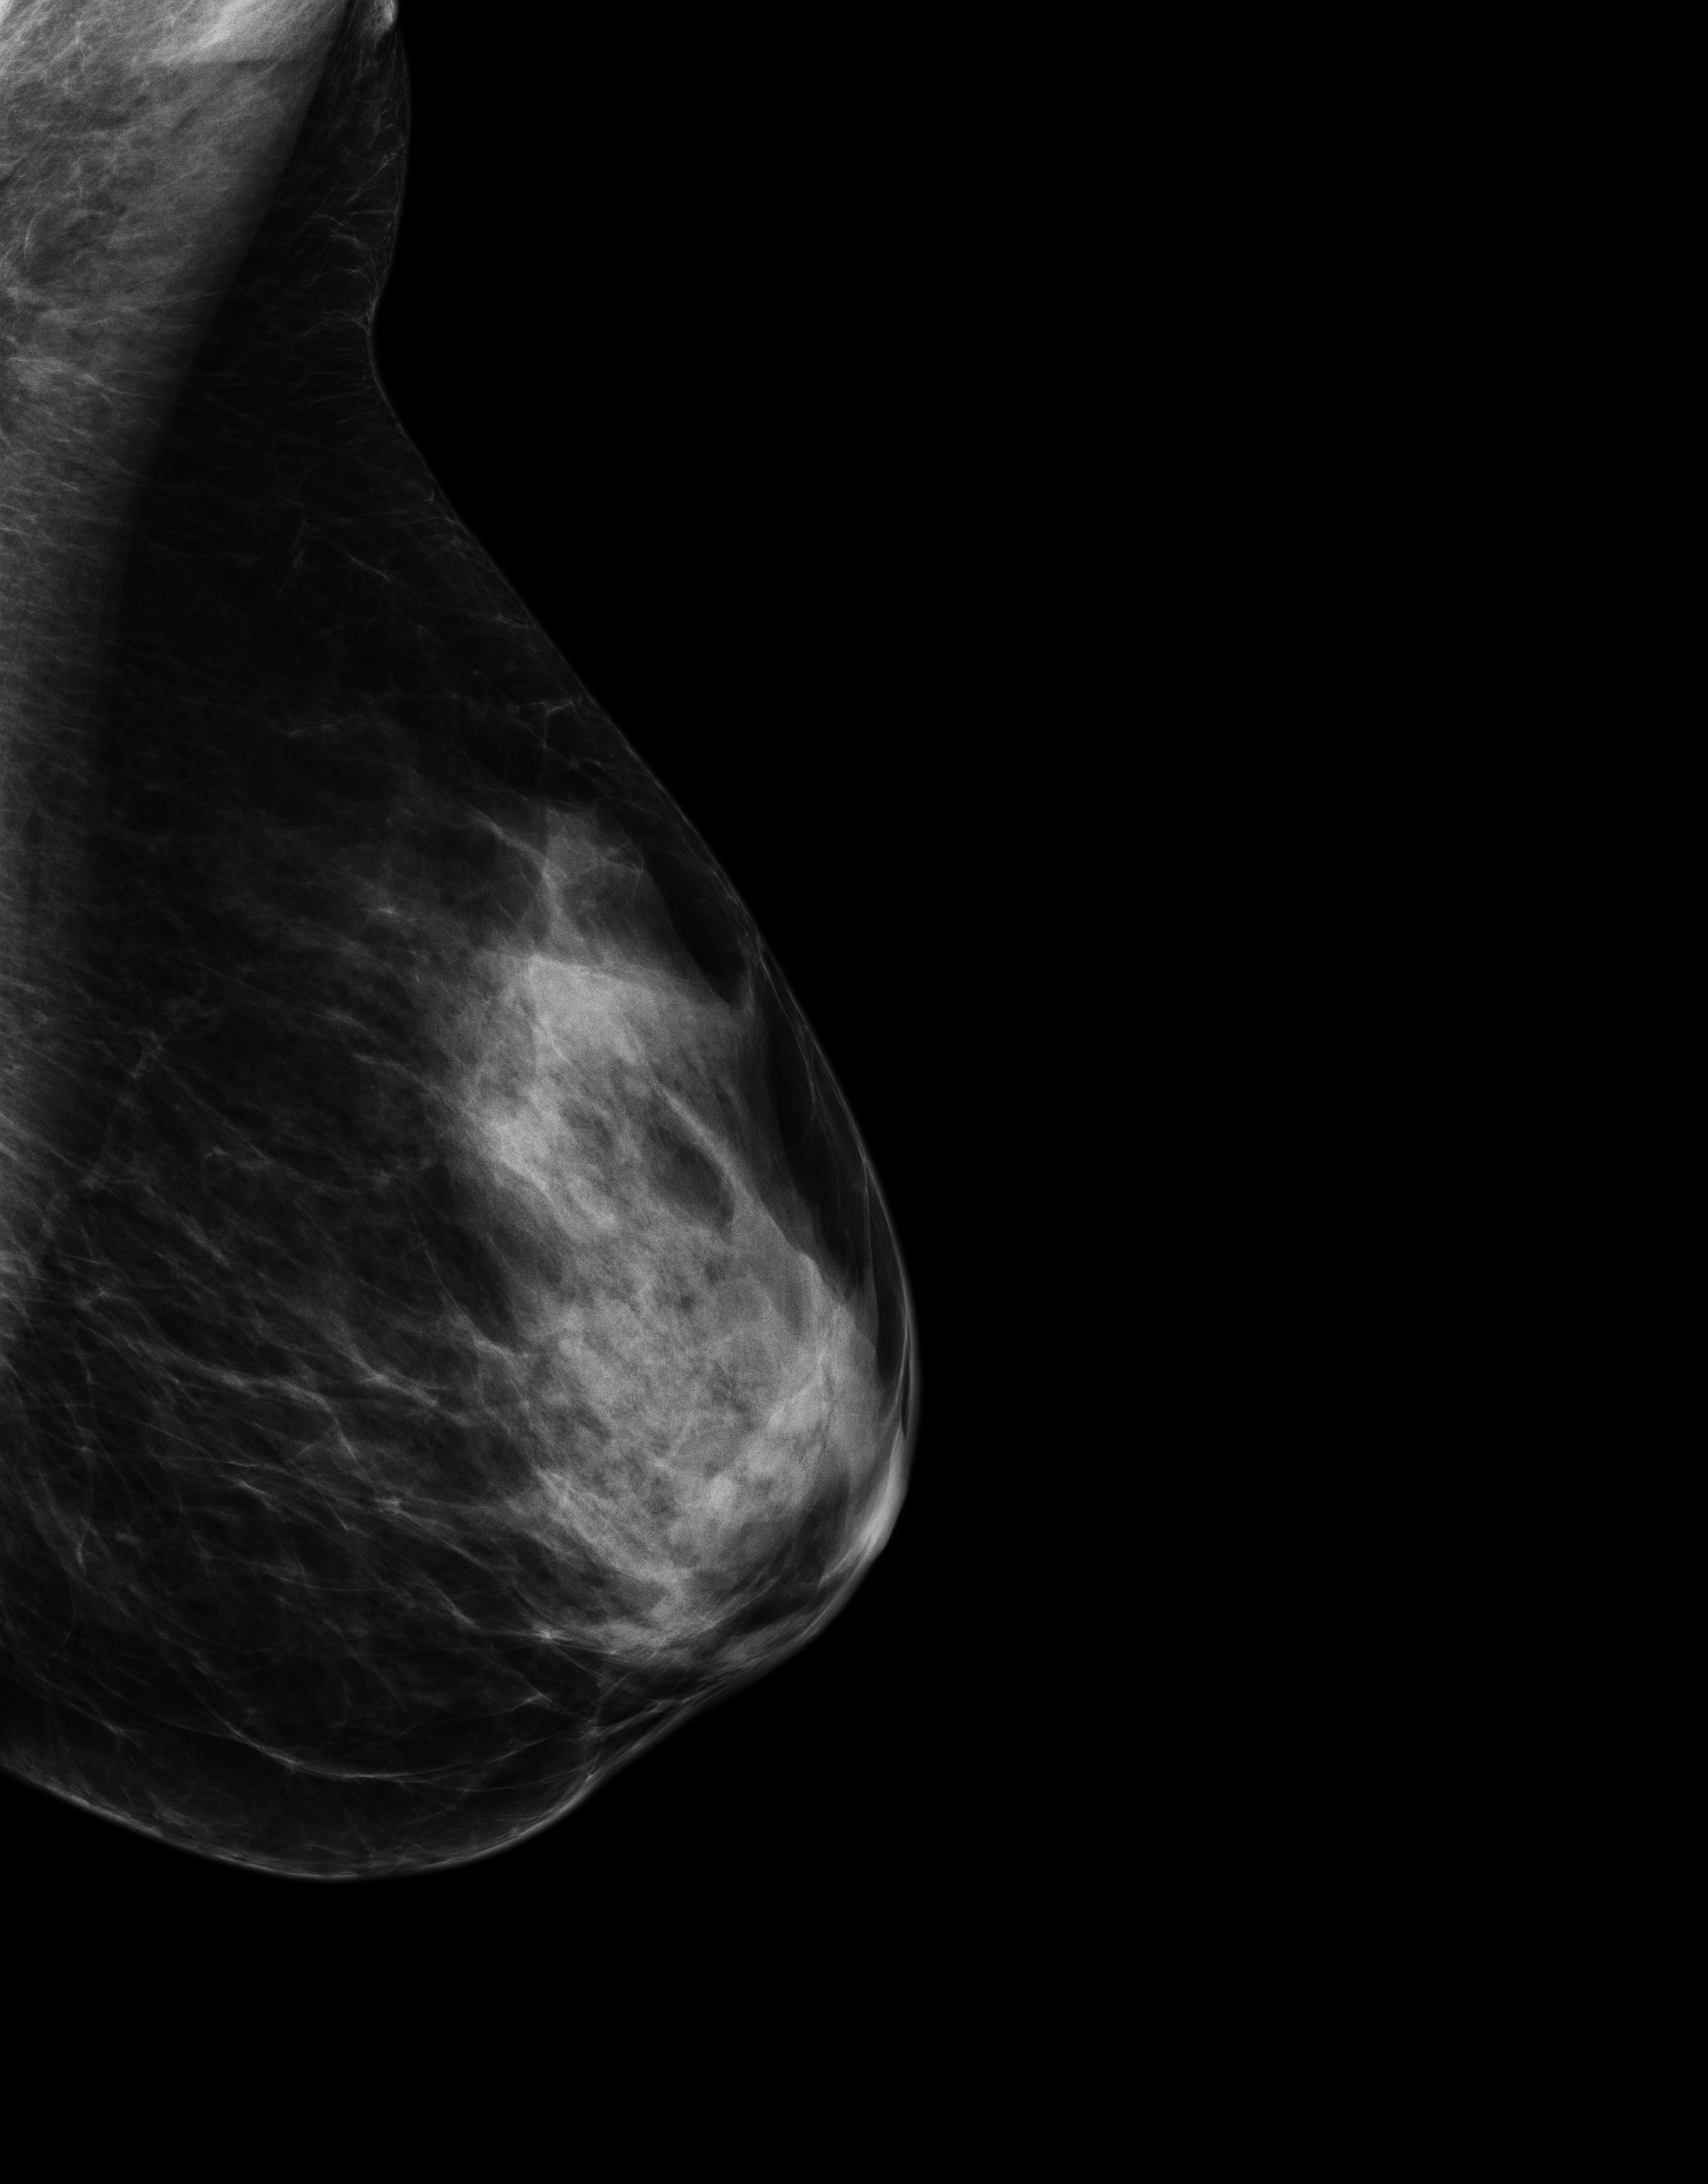
Annual screening mammography examination. Patient: female, 49 years.
Image type: full-field digital mammogram. Breast: left. Projection: mediolateral oblique (MLO) view.